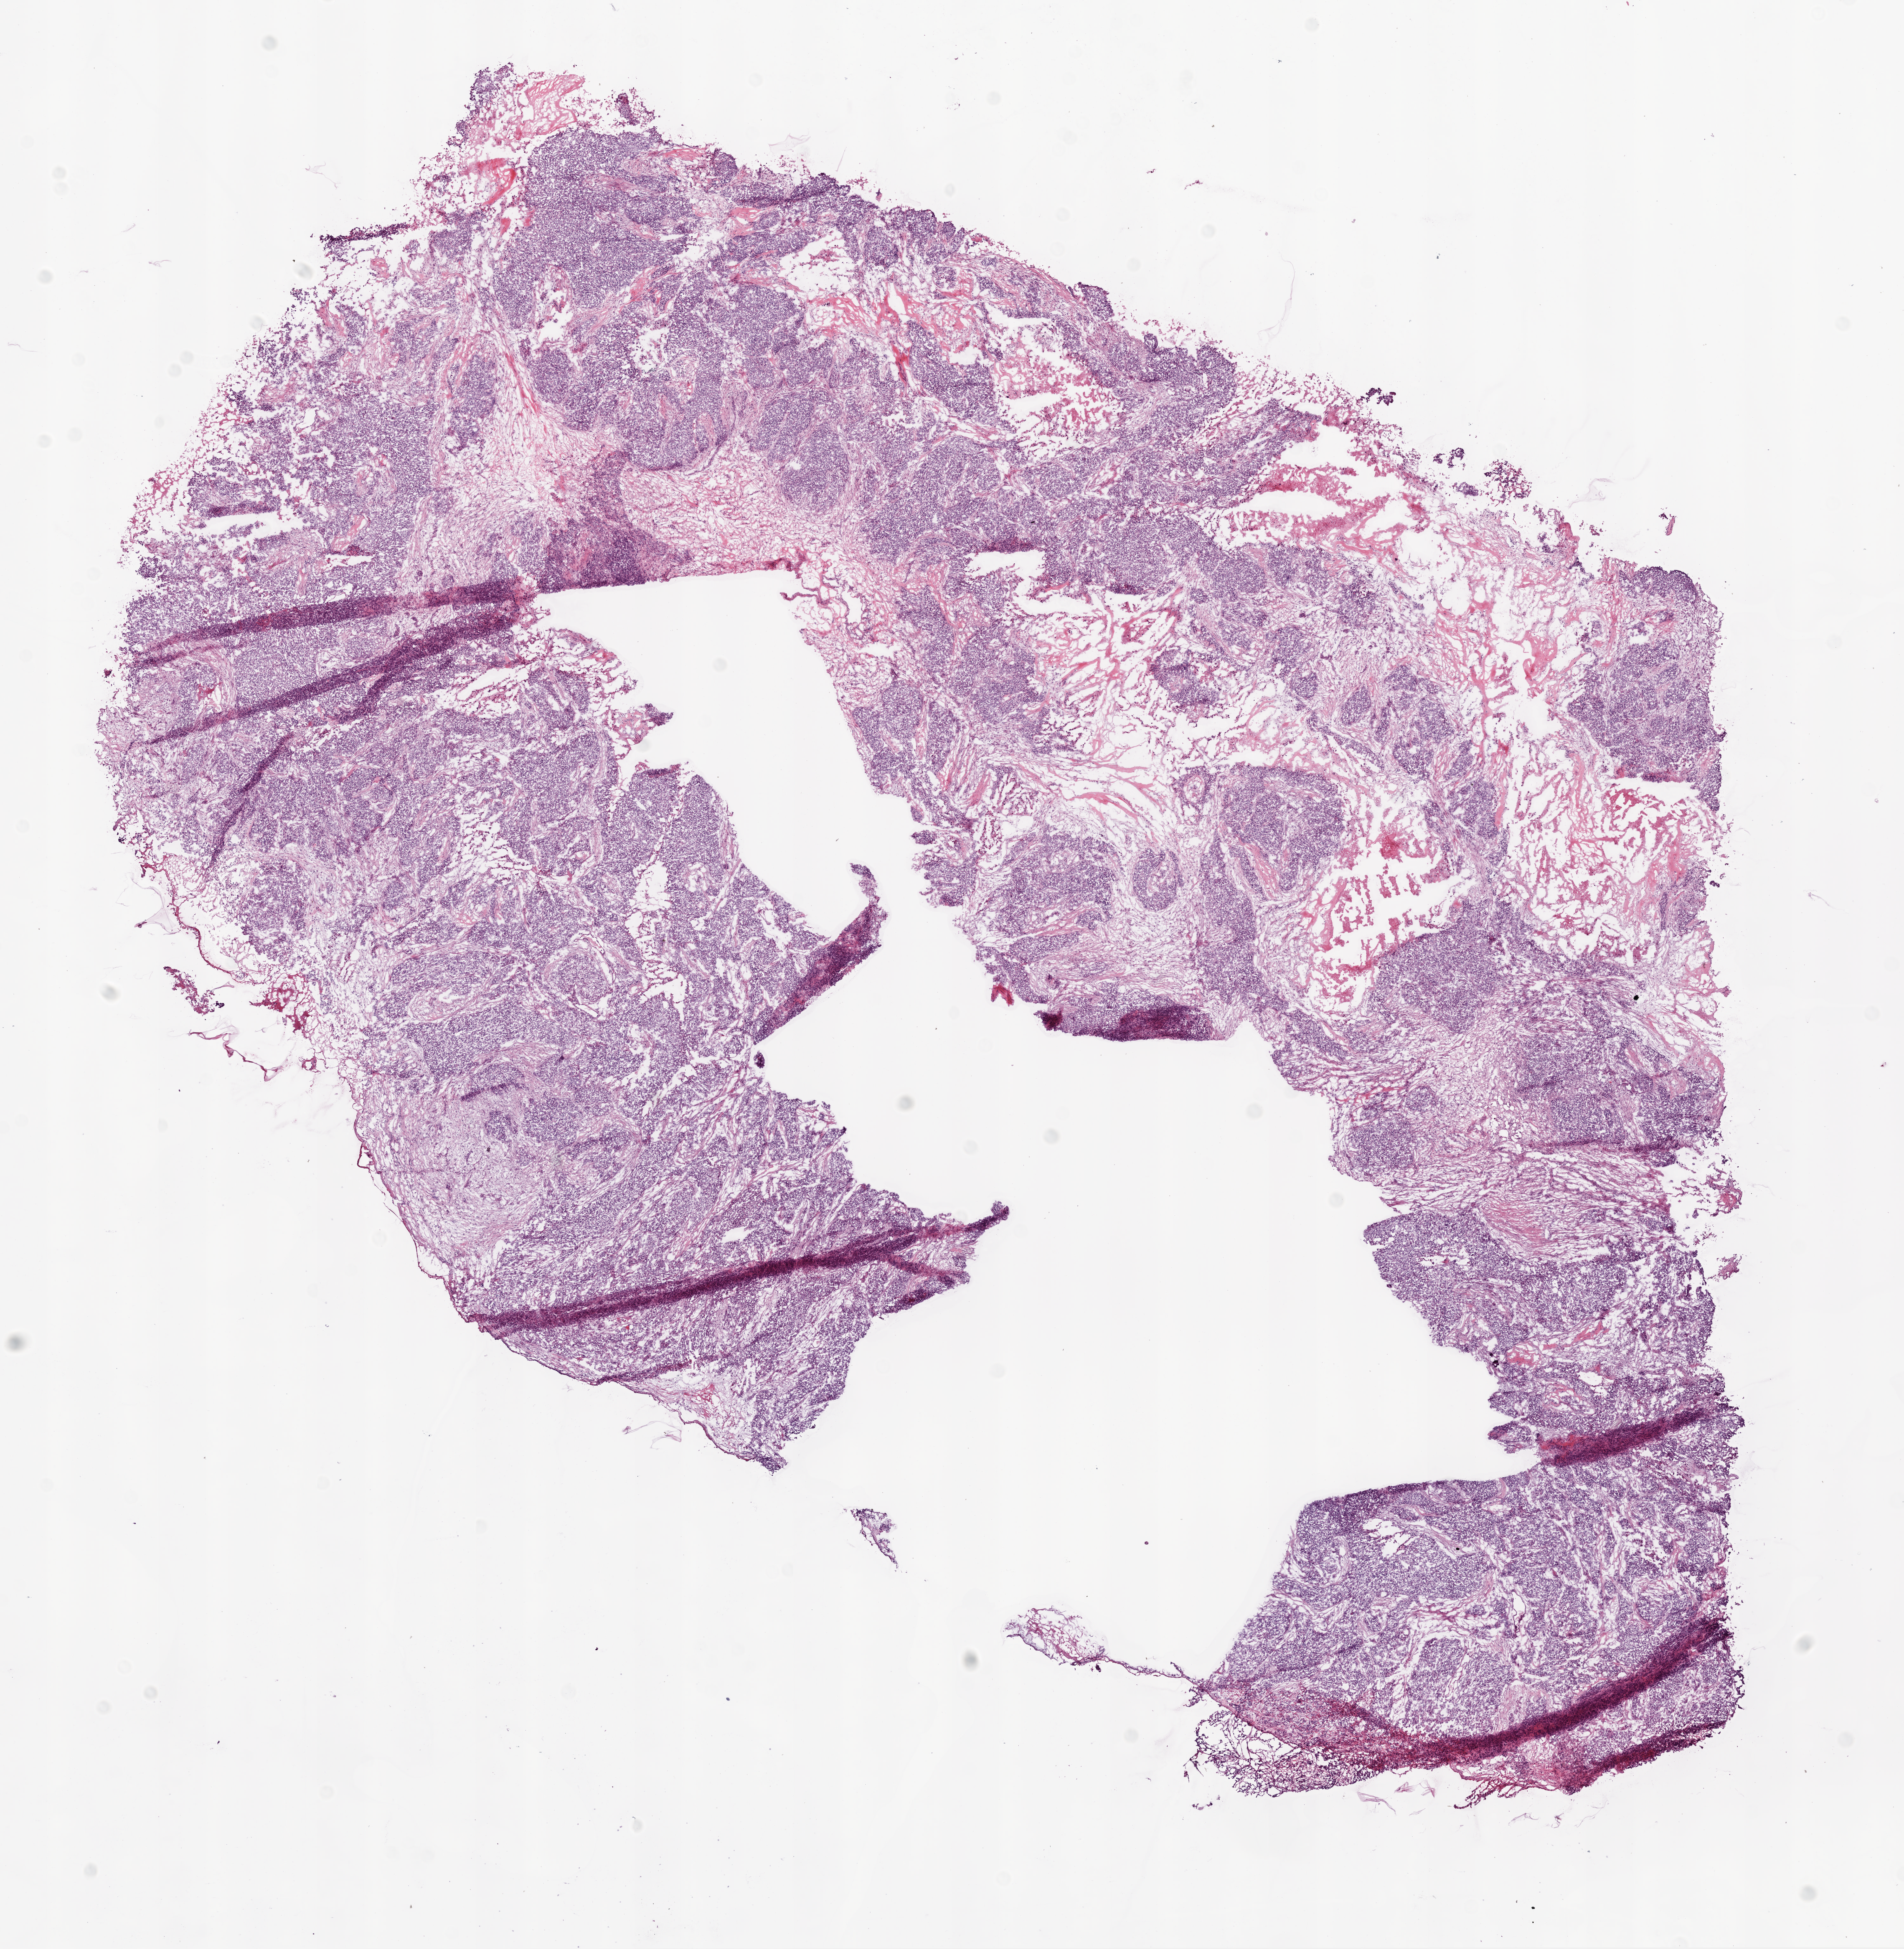
Hematoxylin and eosin (H&E) stained whole-slide image, shown as a low-resolution overview of the whole scanned area (about 12.0 x 12.3 mm, from a 20x scan); frozen section from the bottom of the tissue portion; primary tumour sample from the ovary. Patient: female, age at initial diagnosis 47 years. Histologic grade: G2 (moderately differentiated). Slide review estimates, as recorded: tumour cells 75%, tumour nuclei 80%, normal cells 0%, stromal cells 25%, necrosis 0%. Infiltration values recorded for this section: lymphocyte infiltration 5%.
* FIGO stage: IIIC
* pathologic diagnosis: Serous cystadenocarcinoma, NOS